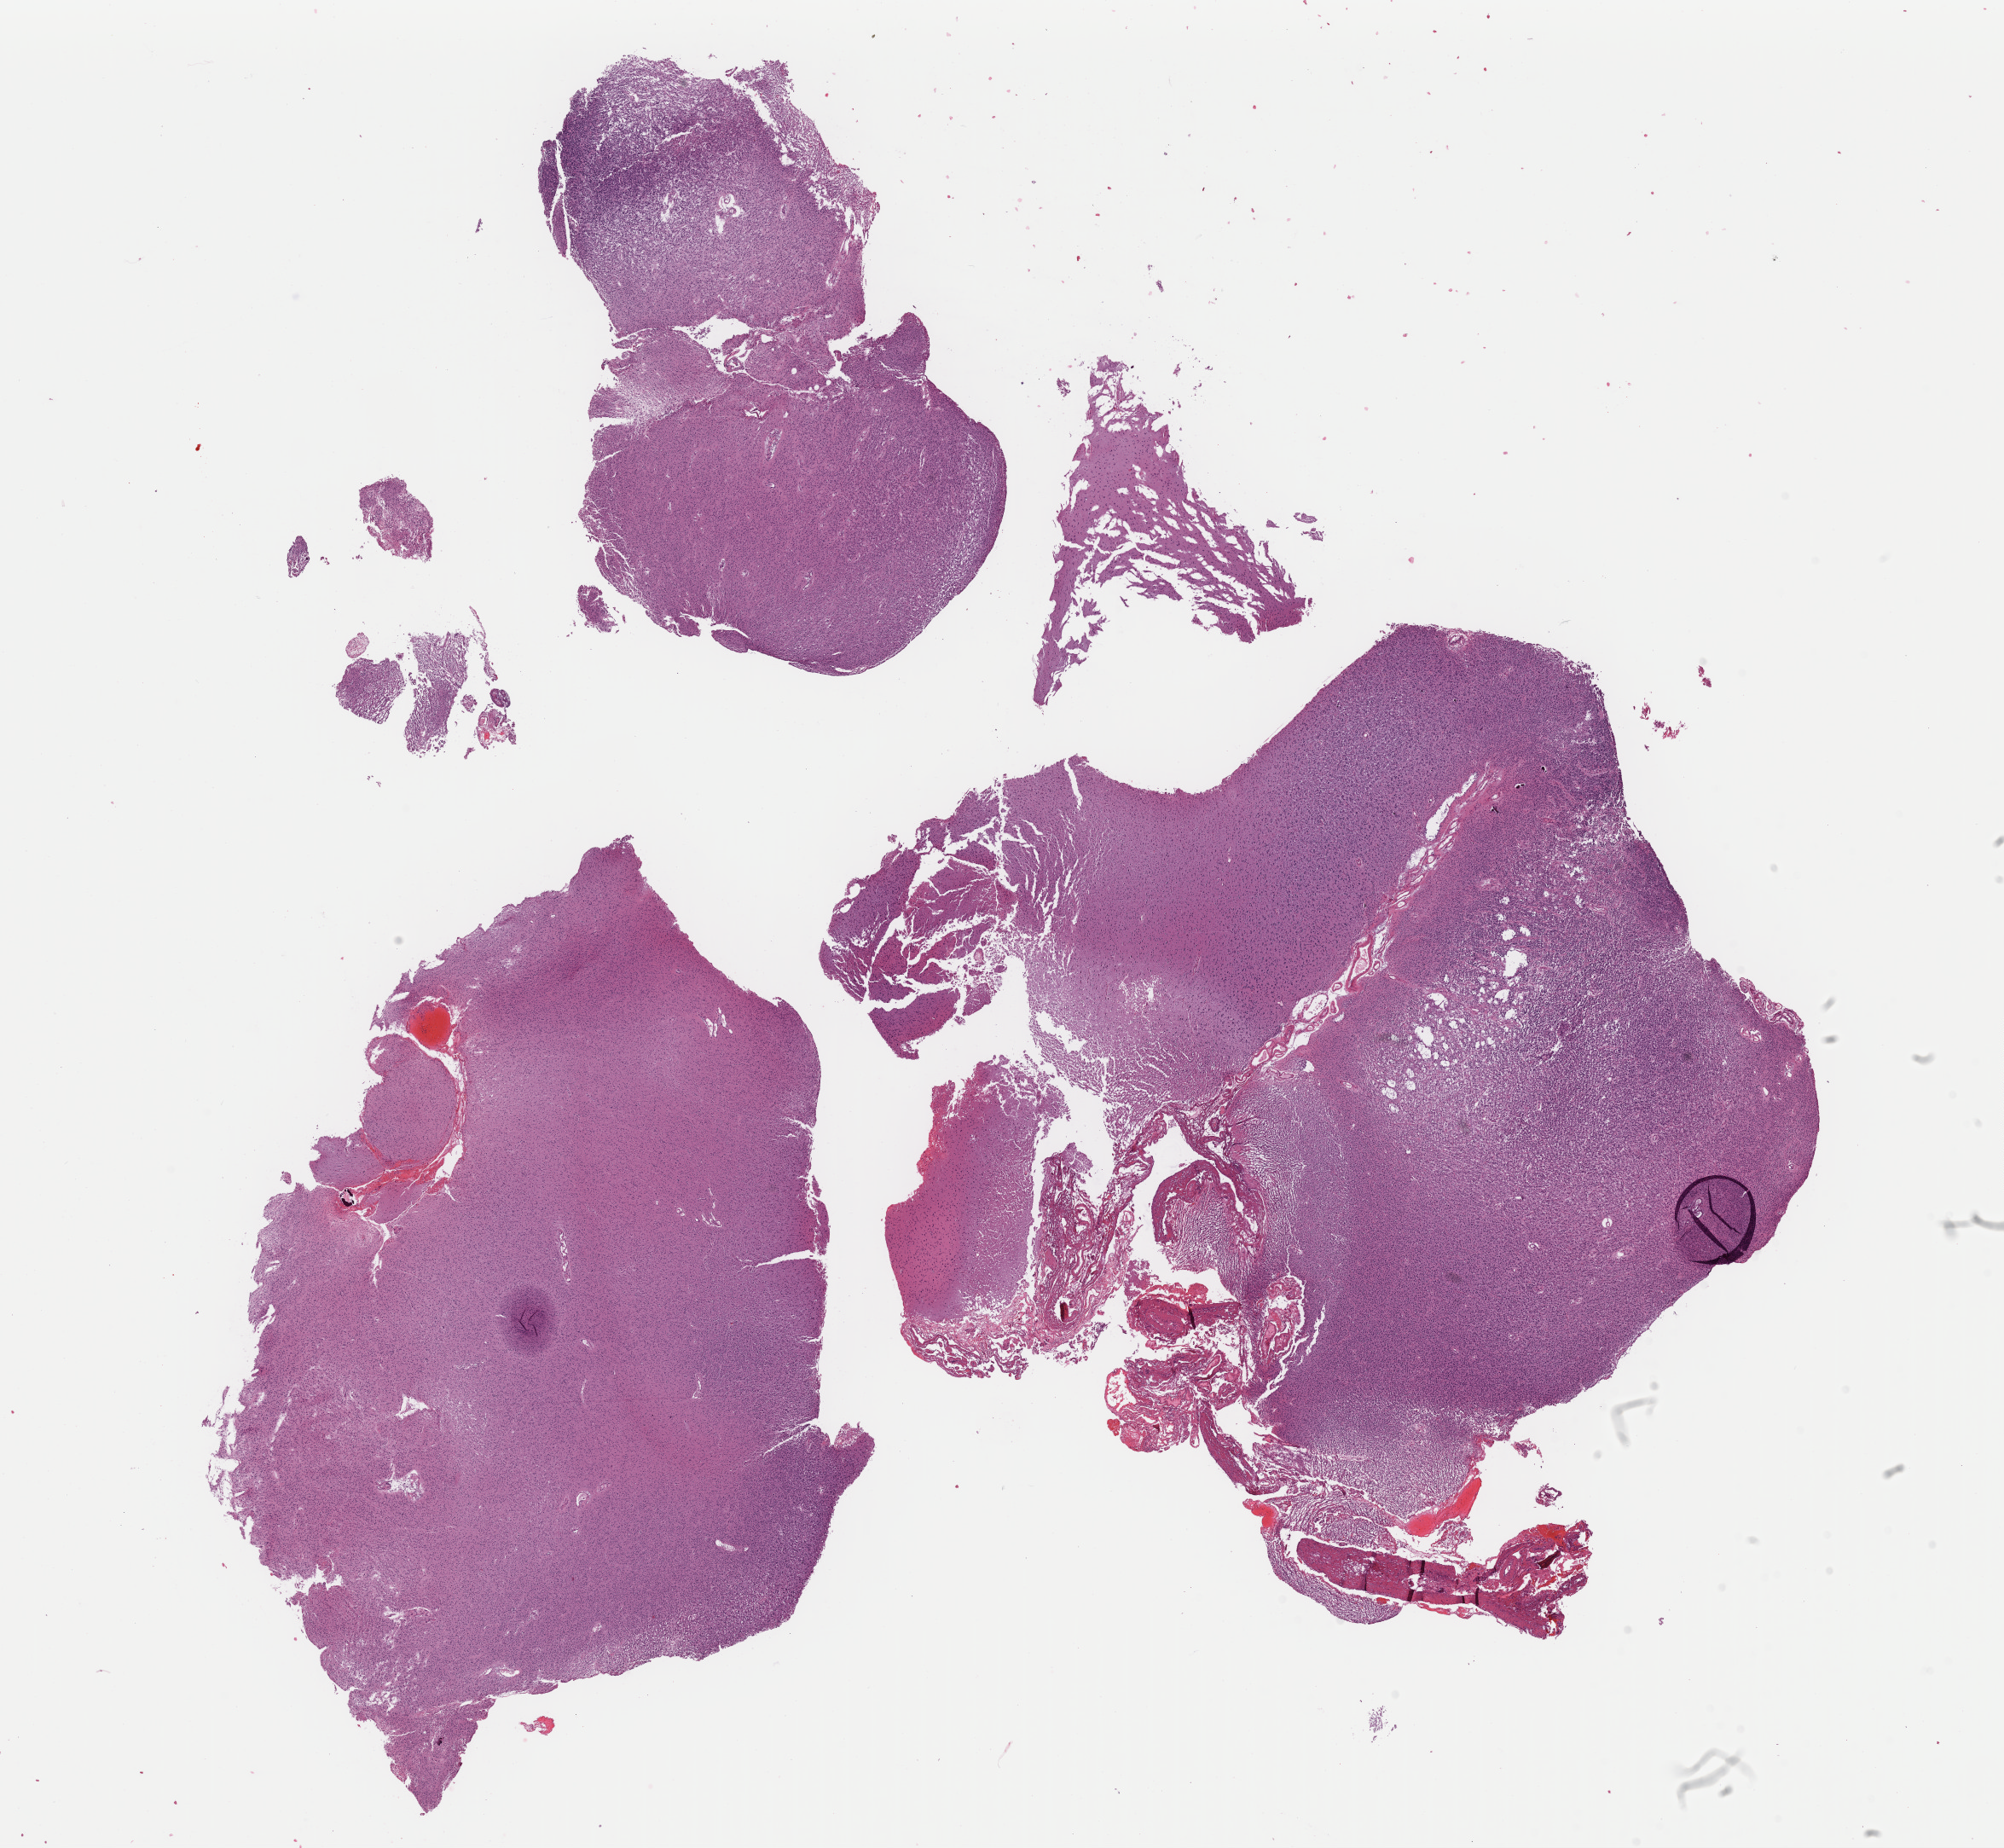
H&E-stained whole-slide image — whole scanned area (about 18.6 x 17.1 mm, from a 40x scan) shown as a low-resolution overview, FFPE section, sample: primary tumour, brain. Female, age 51 years at initial diagnosis. Histologic grade: G3 (poorly differentiated).
Histologic diagnosis: Oligodendroglioma, anaplastic (cerebrum).